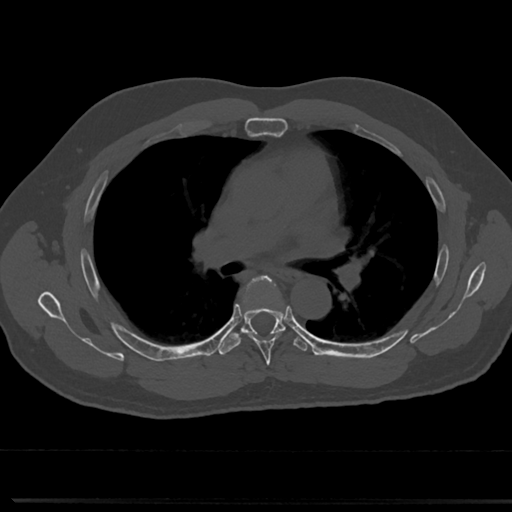
CT including the spine, one axial slice. Position 476 of 817 along the scan axis. Reconstruction kernel Br40s/3. 120 kVp. Bone window (W 1800 / L 400 HU). 512 × 512 image matrix, field of view 355 × 355 mm. Patient: male, 61 years. From the clinical record (not read from this slice): primary cancer: prostate.
Annotated regions visible in this slice (semi-automatically segmented with operator editing):
- T5 vertebra: bounding box (x1, y1, x2, y2) in pixels: (238, 277, 288, 360)
- T6 vertebra: (224, 323, 287, 348)